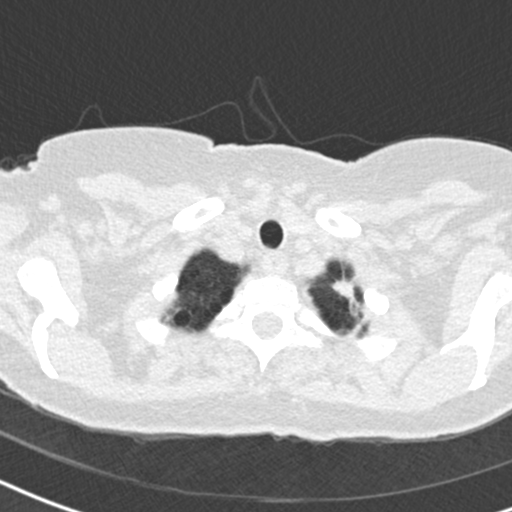
Low-dose screening chest CT, one axial slice; slice 174 of 184 in the series (ordered by position); lung window (W 1500 / L -600 HU); 2 mm slice thickness; 512 × 512 image matrix, field of view 280 × 280 mm.
Annotated regions visible in this slice (outlined manually by an expert reader):
- lesion 1 (tumor, upper lobe of left lung): bounding box (x1, y1, x2, y2) in pixels: (332, 275, 355, 299)